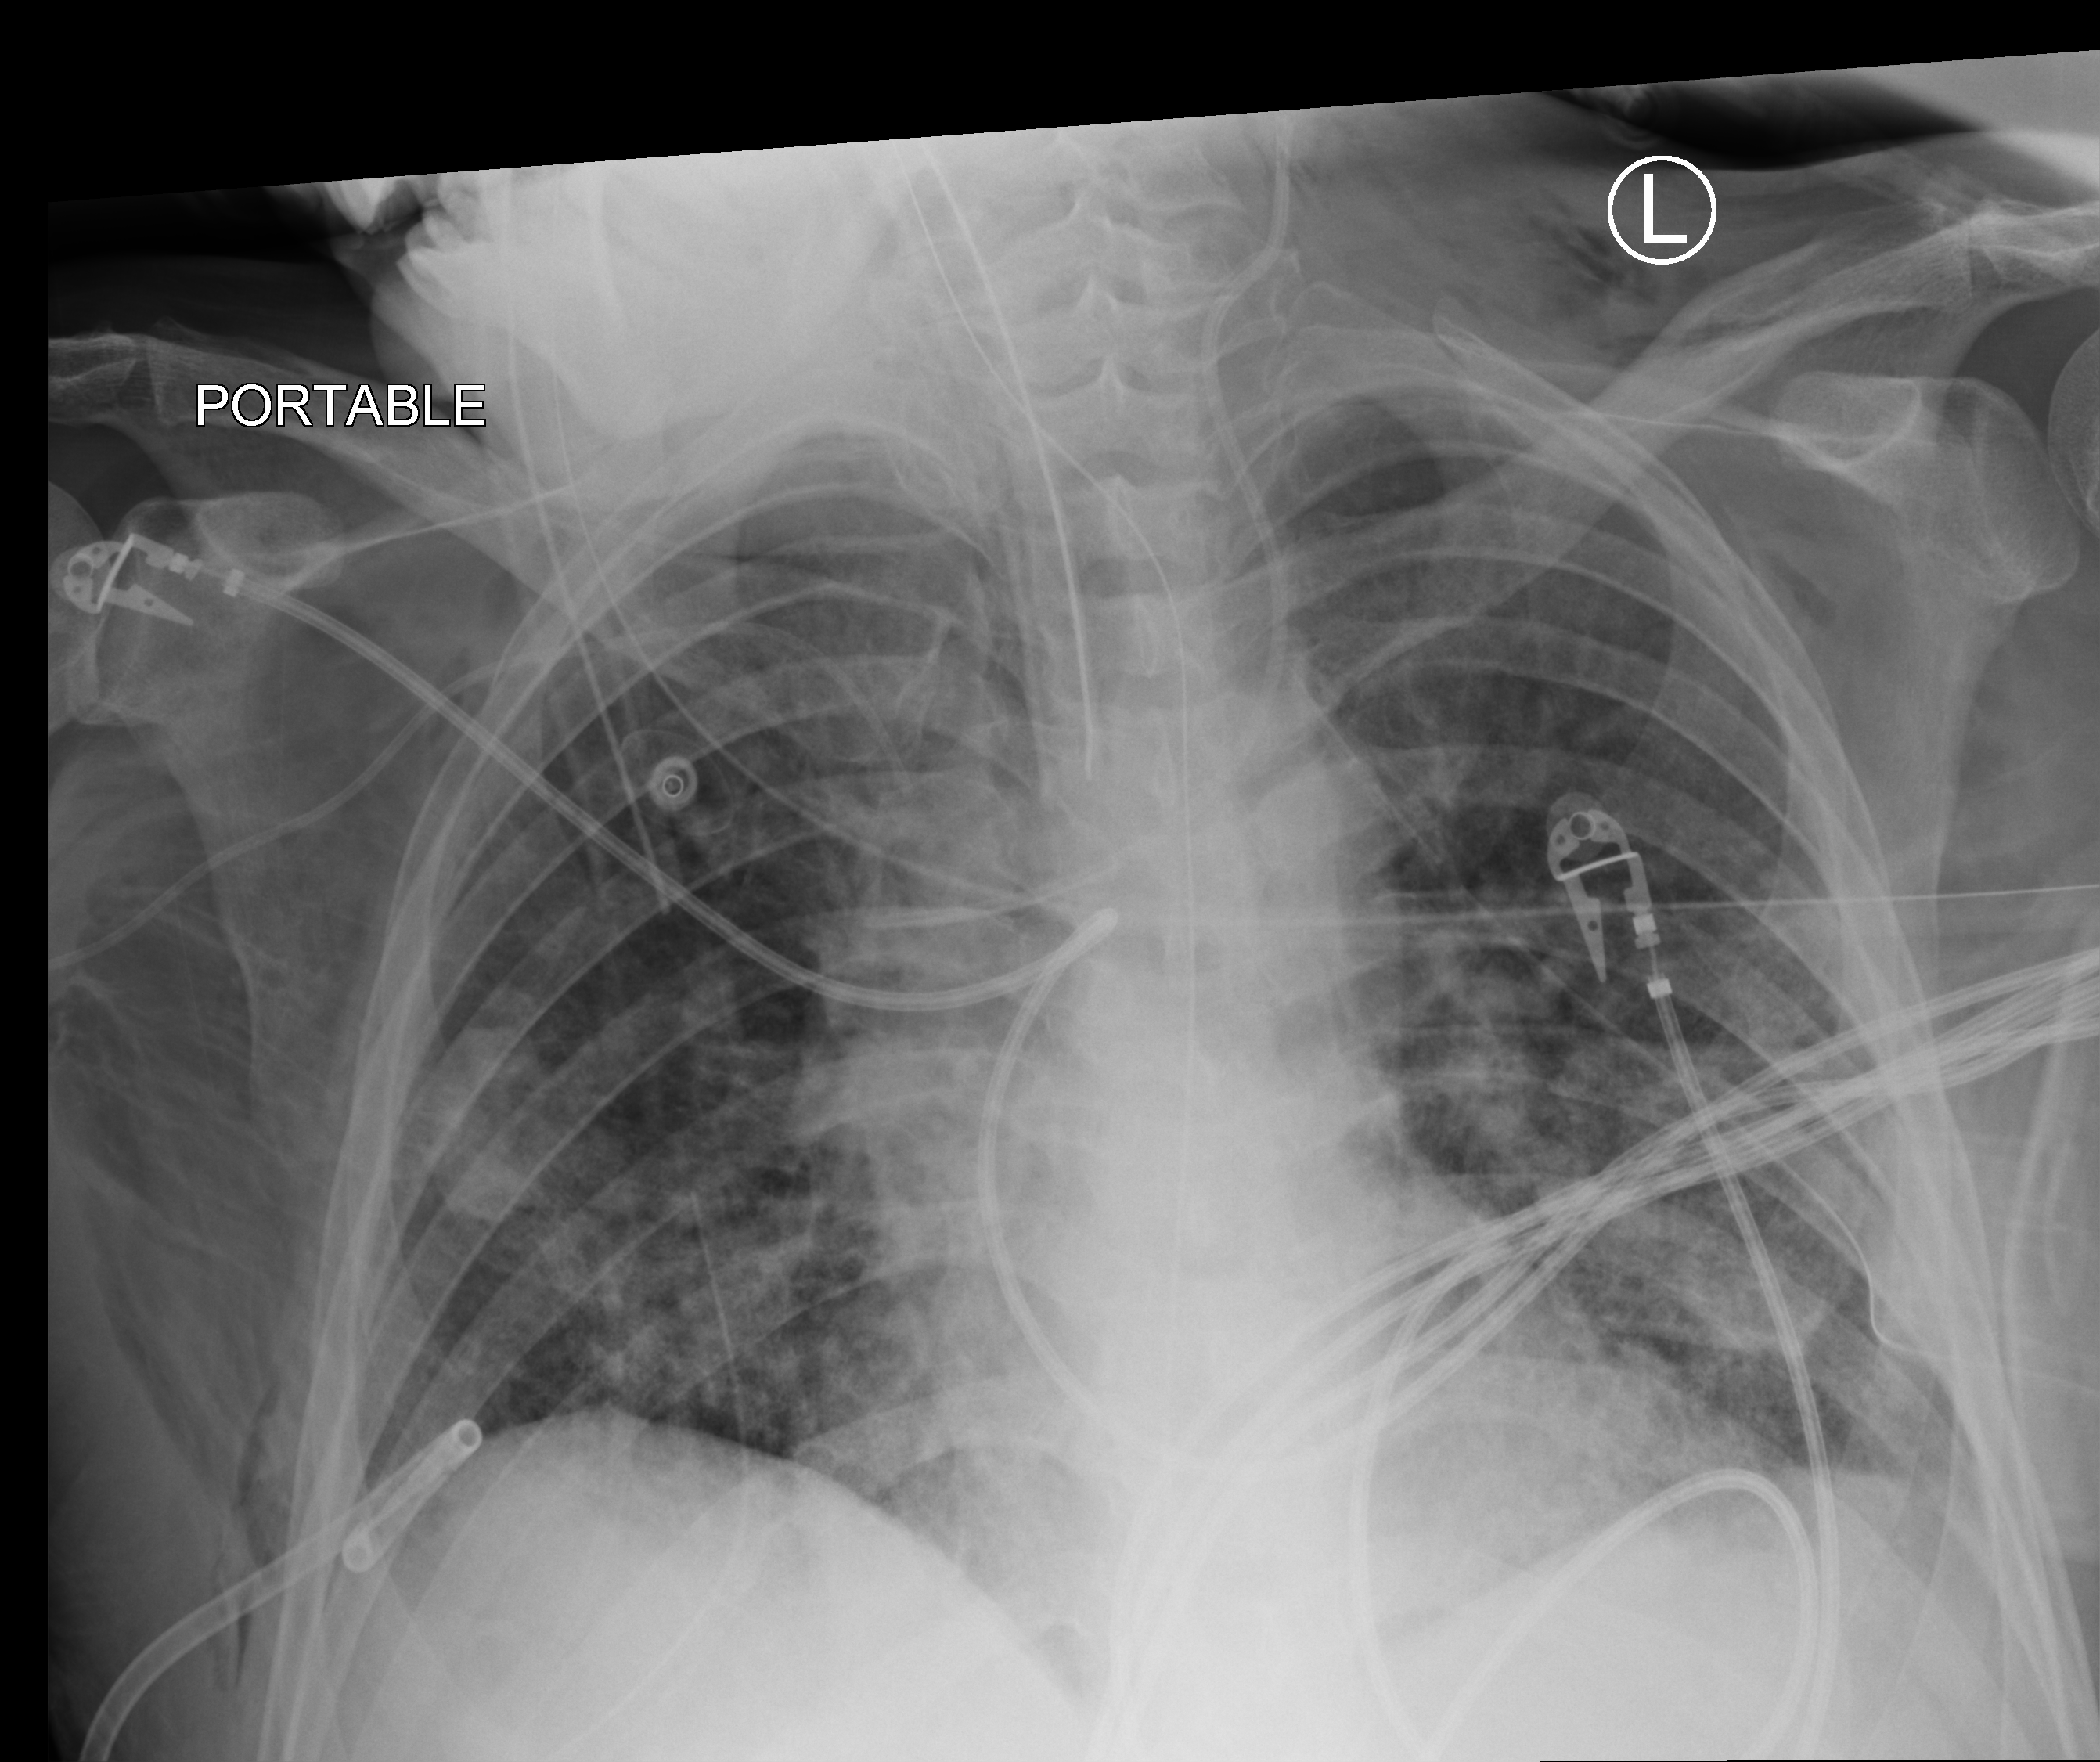
Chest X-ray (portable). Patient hospitalised with COVID-19; male, aged 18–59 years.
Hospital-stay facts (about this admission, not read from this image; timing relative to this image not recorded):
- COPD (admission record): no
- length of hospital stay: 77 days
- admitted to intensive care during this hospital stay: yes